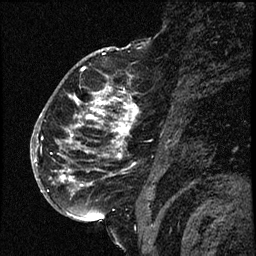
Breast MRI (dynamic contrast-enhanced), one sagittal slice. Dynamic contrast-enhanced study with each time point stored as its own series, time point 2 of 3 at this slice position (early post-contrast, ordered by acquisition time). 1.5 T. TE 4.2 ms, TR 17.6 ms. 256 × 256 image matrix. Female patient. Case-level facts recorded for this patient, not image findings: setting: breast cancer imaged before/during neoadjuvant chemotherapy; receptor status: HER2-positive.
Outlined on this slice (semi-automatic segmentation, software-assisted and operator-edited):
- analysis volume of interest (the breast-tissue region the enhancement analysis was run in; not a lesion): bounding box [x1, y1, x2, y2] px = [52, 69, 147, 209]
- tumour enhancement mask (voxels above the 100 % enhancement threshold inside the analysis volume of interest): [59, 87, 139, 187]